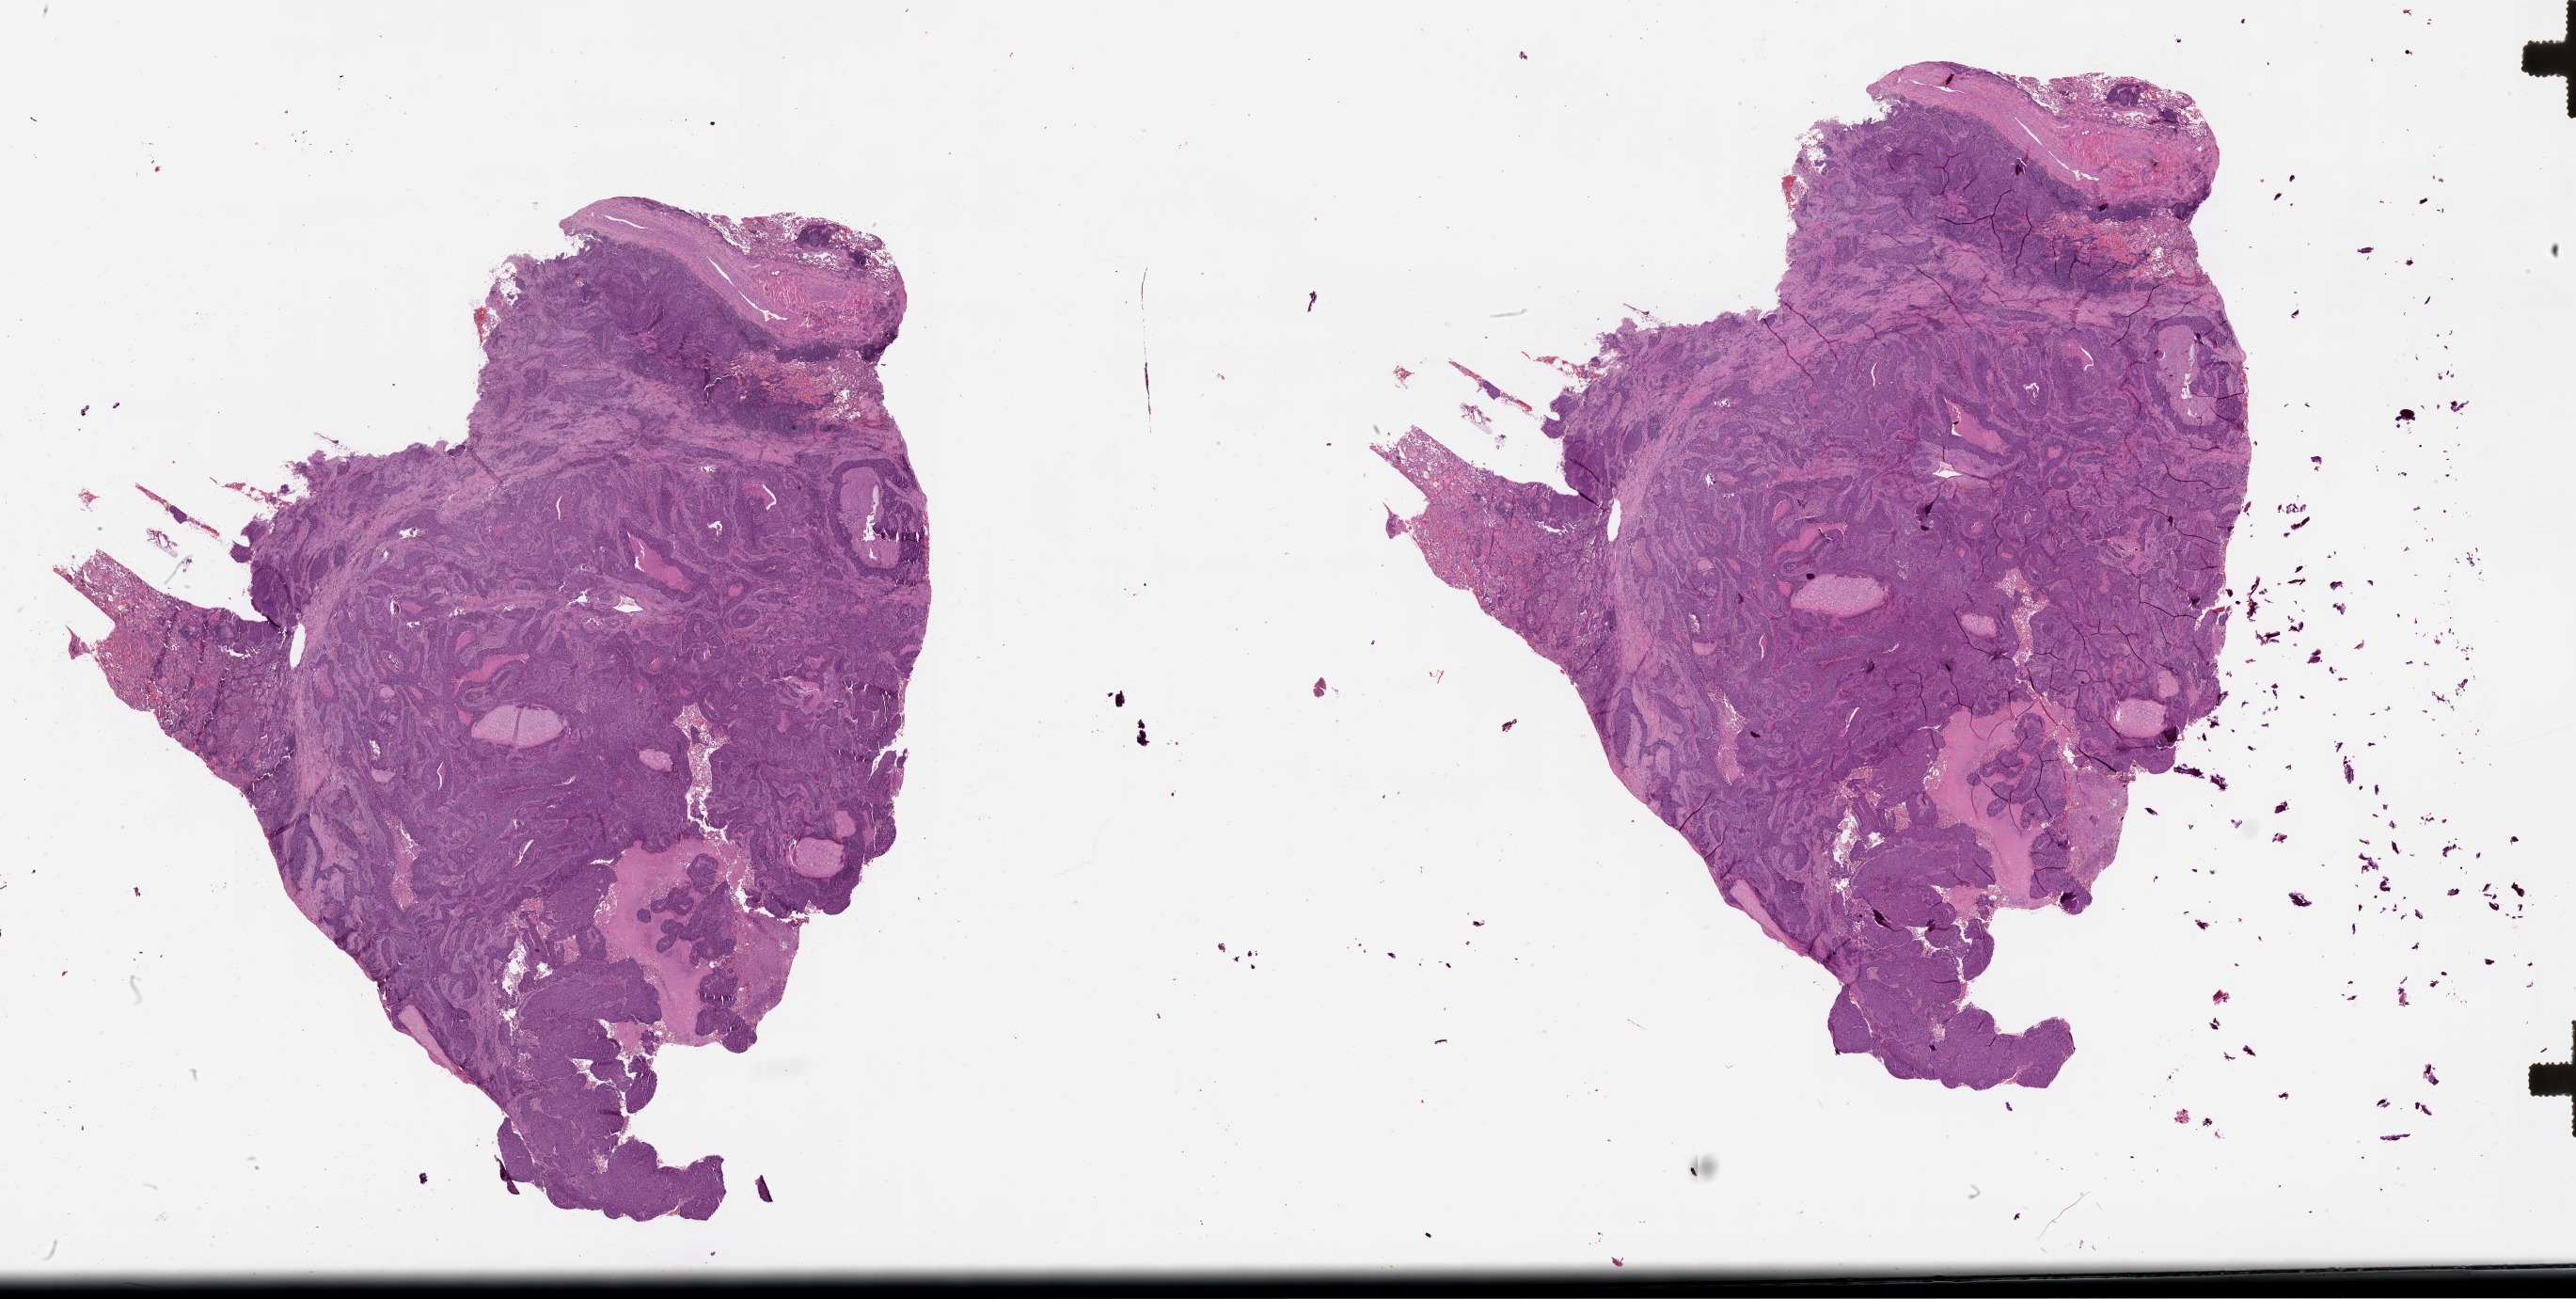
Whole-slide histology image, Hematoxylin and eosin (H&E) stained, whole scanned area (about 44.1 x 22.2 mm, acquisition: 20x scan) shown as a low-resolution overview, tumour tissue sample, lung. Patient: male, age 58 years.
• patient diagnosis (cohort enrolment): squamous cell carcinoma (lung)